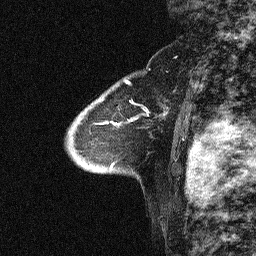
Breast MRI (dynamic contrast-enhanced), one sagittal slice. Slice 45 of 64 in the series (ordered by position). Dynamic contrast-enhanced study with each time point stored as its own series, time point 2 of 3 at this slice position (early post-contrast, ordered by acquisition time). 1.5 T. TE 4.5 ms, TR 11 ms. 2.06 mm slice thickness. 256 × 256 image matrix. Patient: female, 46 years. Case-level facts recorded for this patient, not image findings: setting: breast cancer imaged before/during neoadjuvant chemotherapy; receptor status: HER2-positive.
Outlined on this slice (semi-automatically segmented with operator editing):
- analysis volume of interest (the breast-tissue region the enhancement analysis was run in; not a lesion): bounding box [x1, y1, x2, y2] px = [47, 51, 180, 169]
- tumour enhancement mask (voxels above the 90 % enhancement threshold inside the analysis volume of interest): [118, 104, 165, 124]